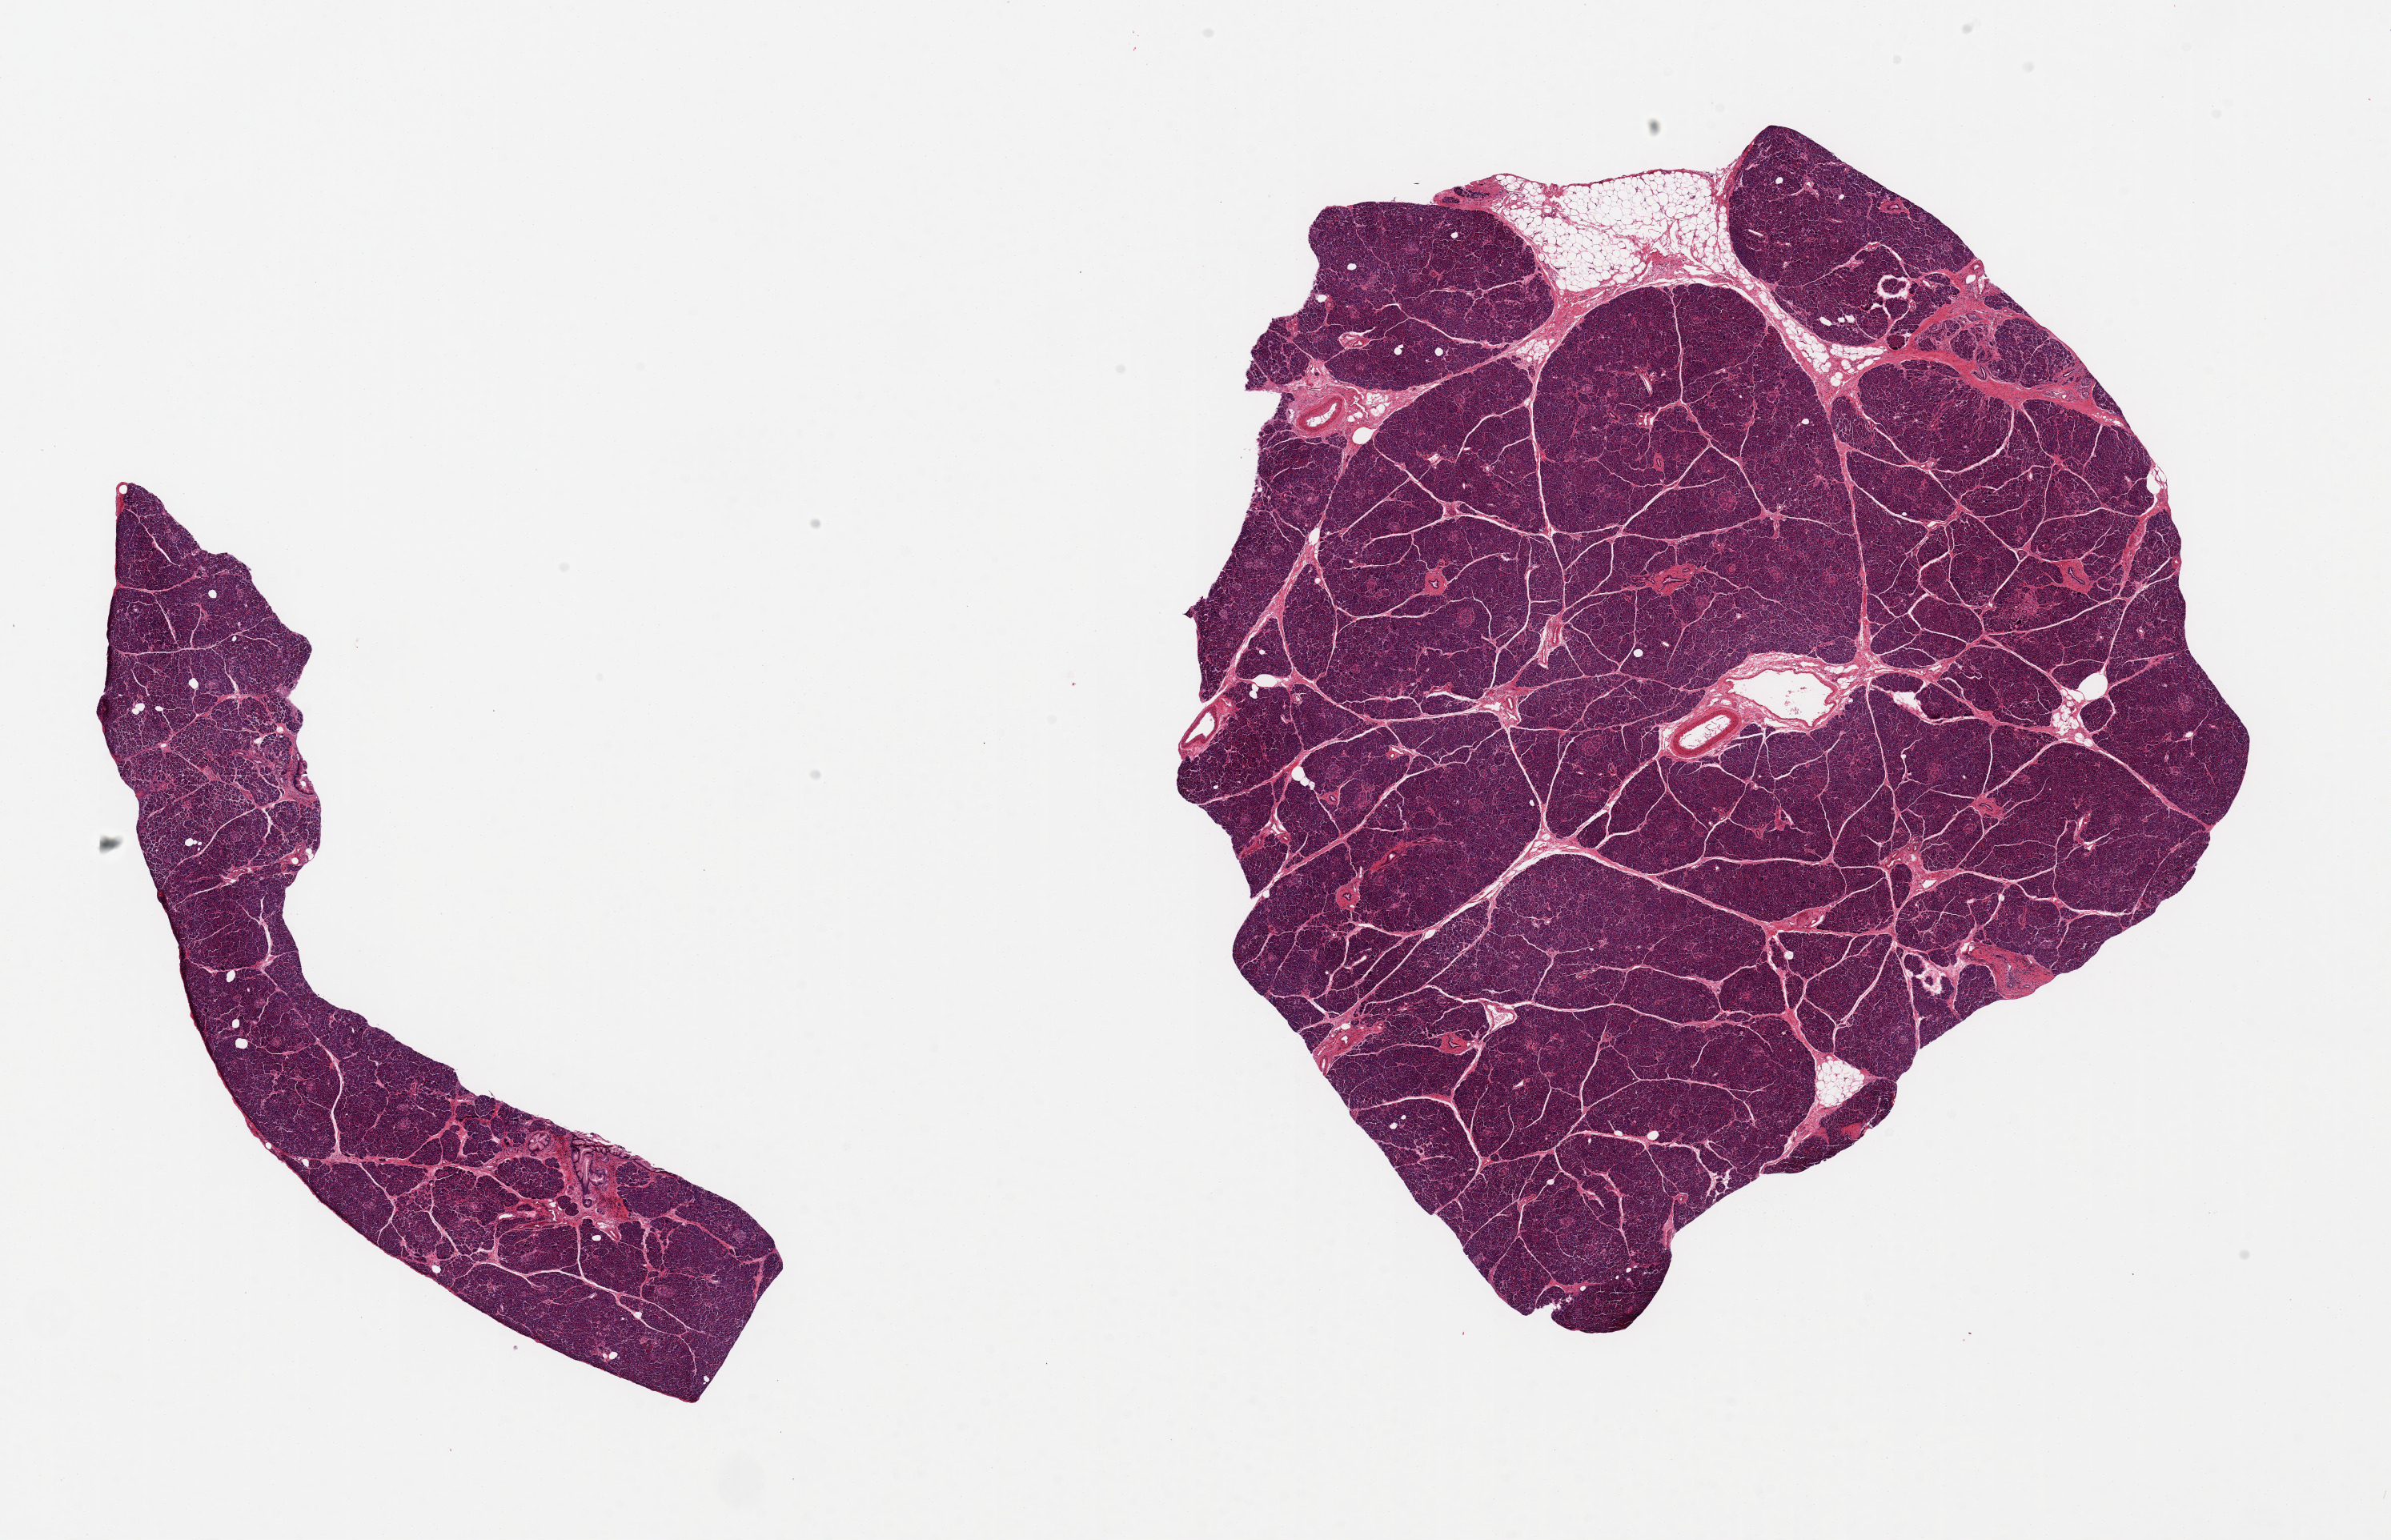
Haematoxylin and eosin whole-slide image, brightfield, shown as a low-resolution overview of the whole scanned area (about 23.6 x 15.2 mm, acquisition: 20x scan); PAXgene-fixed, paraffin-embedded tissue; sampled site (target tissue): pancreas; tissue donor sample. Donor sex: male.
Pathologist's review note for this sample: 2 pieces 10x9 & 10x2 mm; <10& peripheral adipose; good preservation.